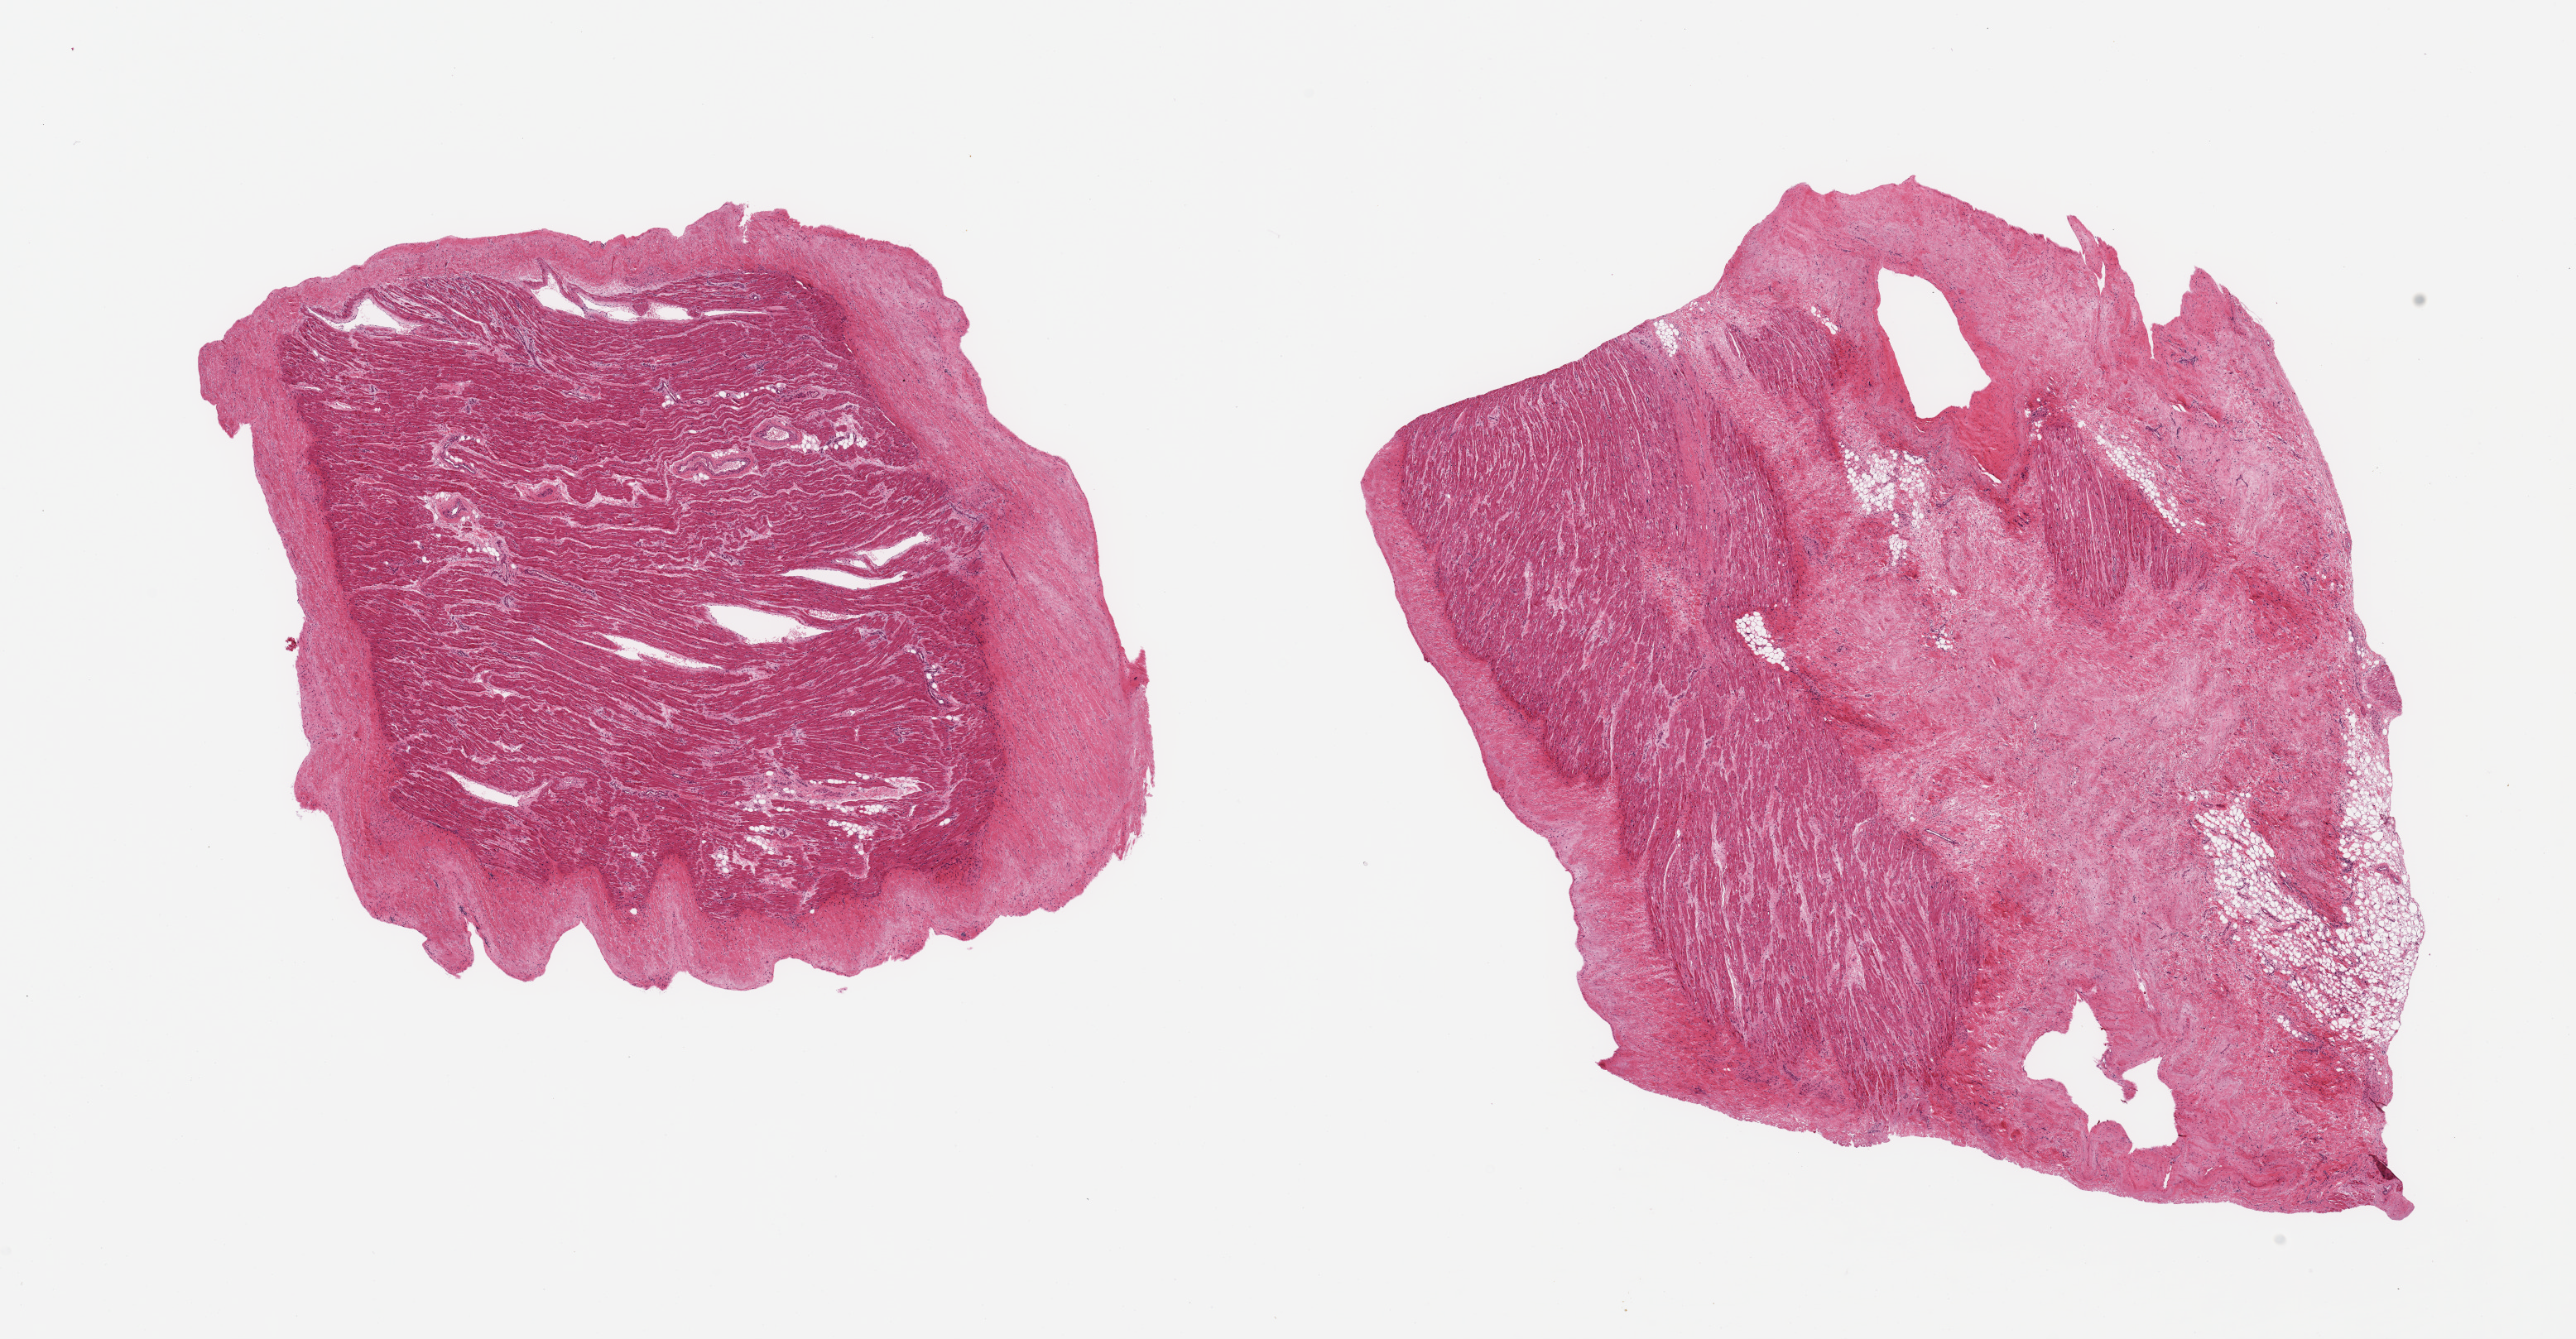
Whole-slide image, haematoxylin and eosin stain — a low-resolution overview of the entire scanned area, about 24.6 x 12.8 mm (from a 20x scan). PAXgene-fixed paraffin-embedded (PFPE) section. Section of auricular appendage (target tissue). Tissue donor sample.
- reviewer comment on this tissue sample: 2 pieces; 1 piece surrounded by up to 1.4mm fibrous subpericardial layer; other has 60% fibrofatty content